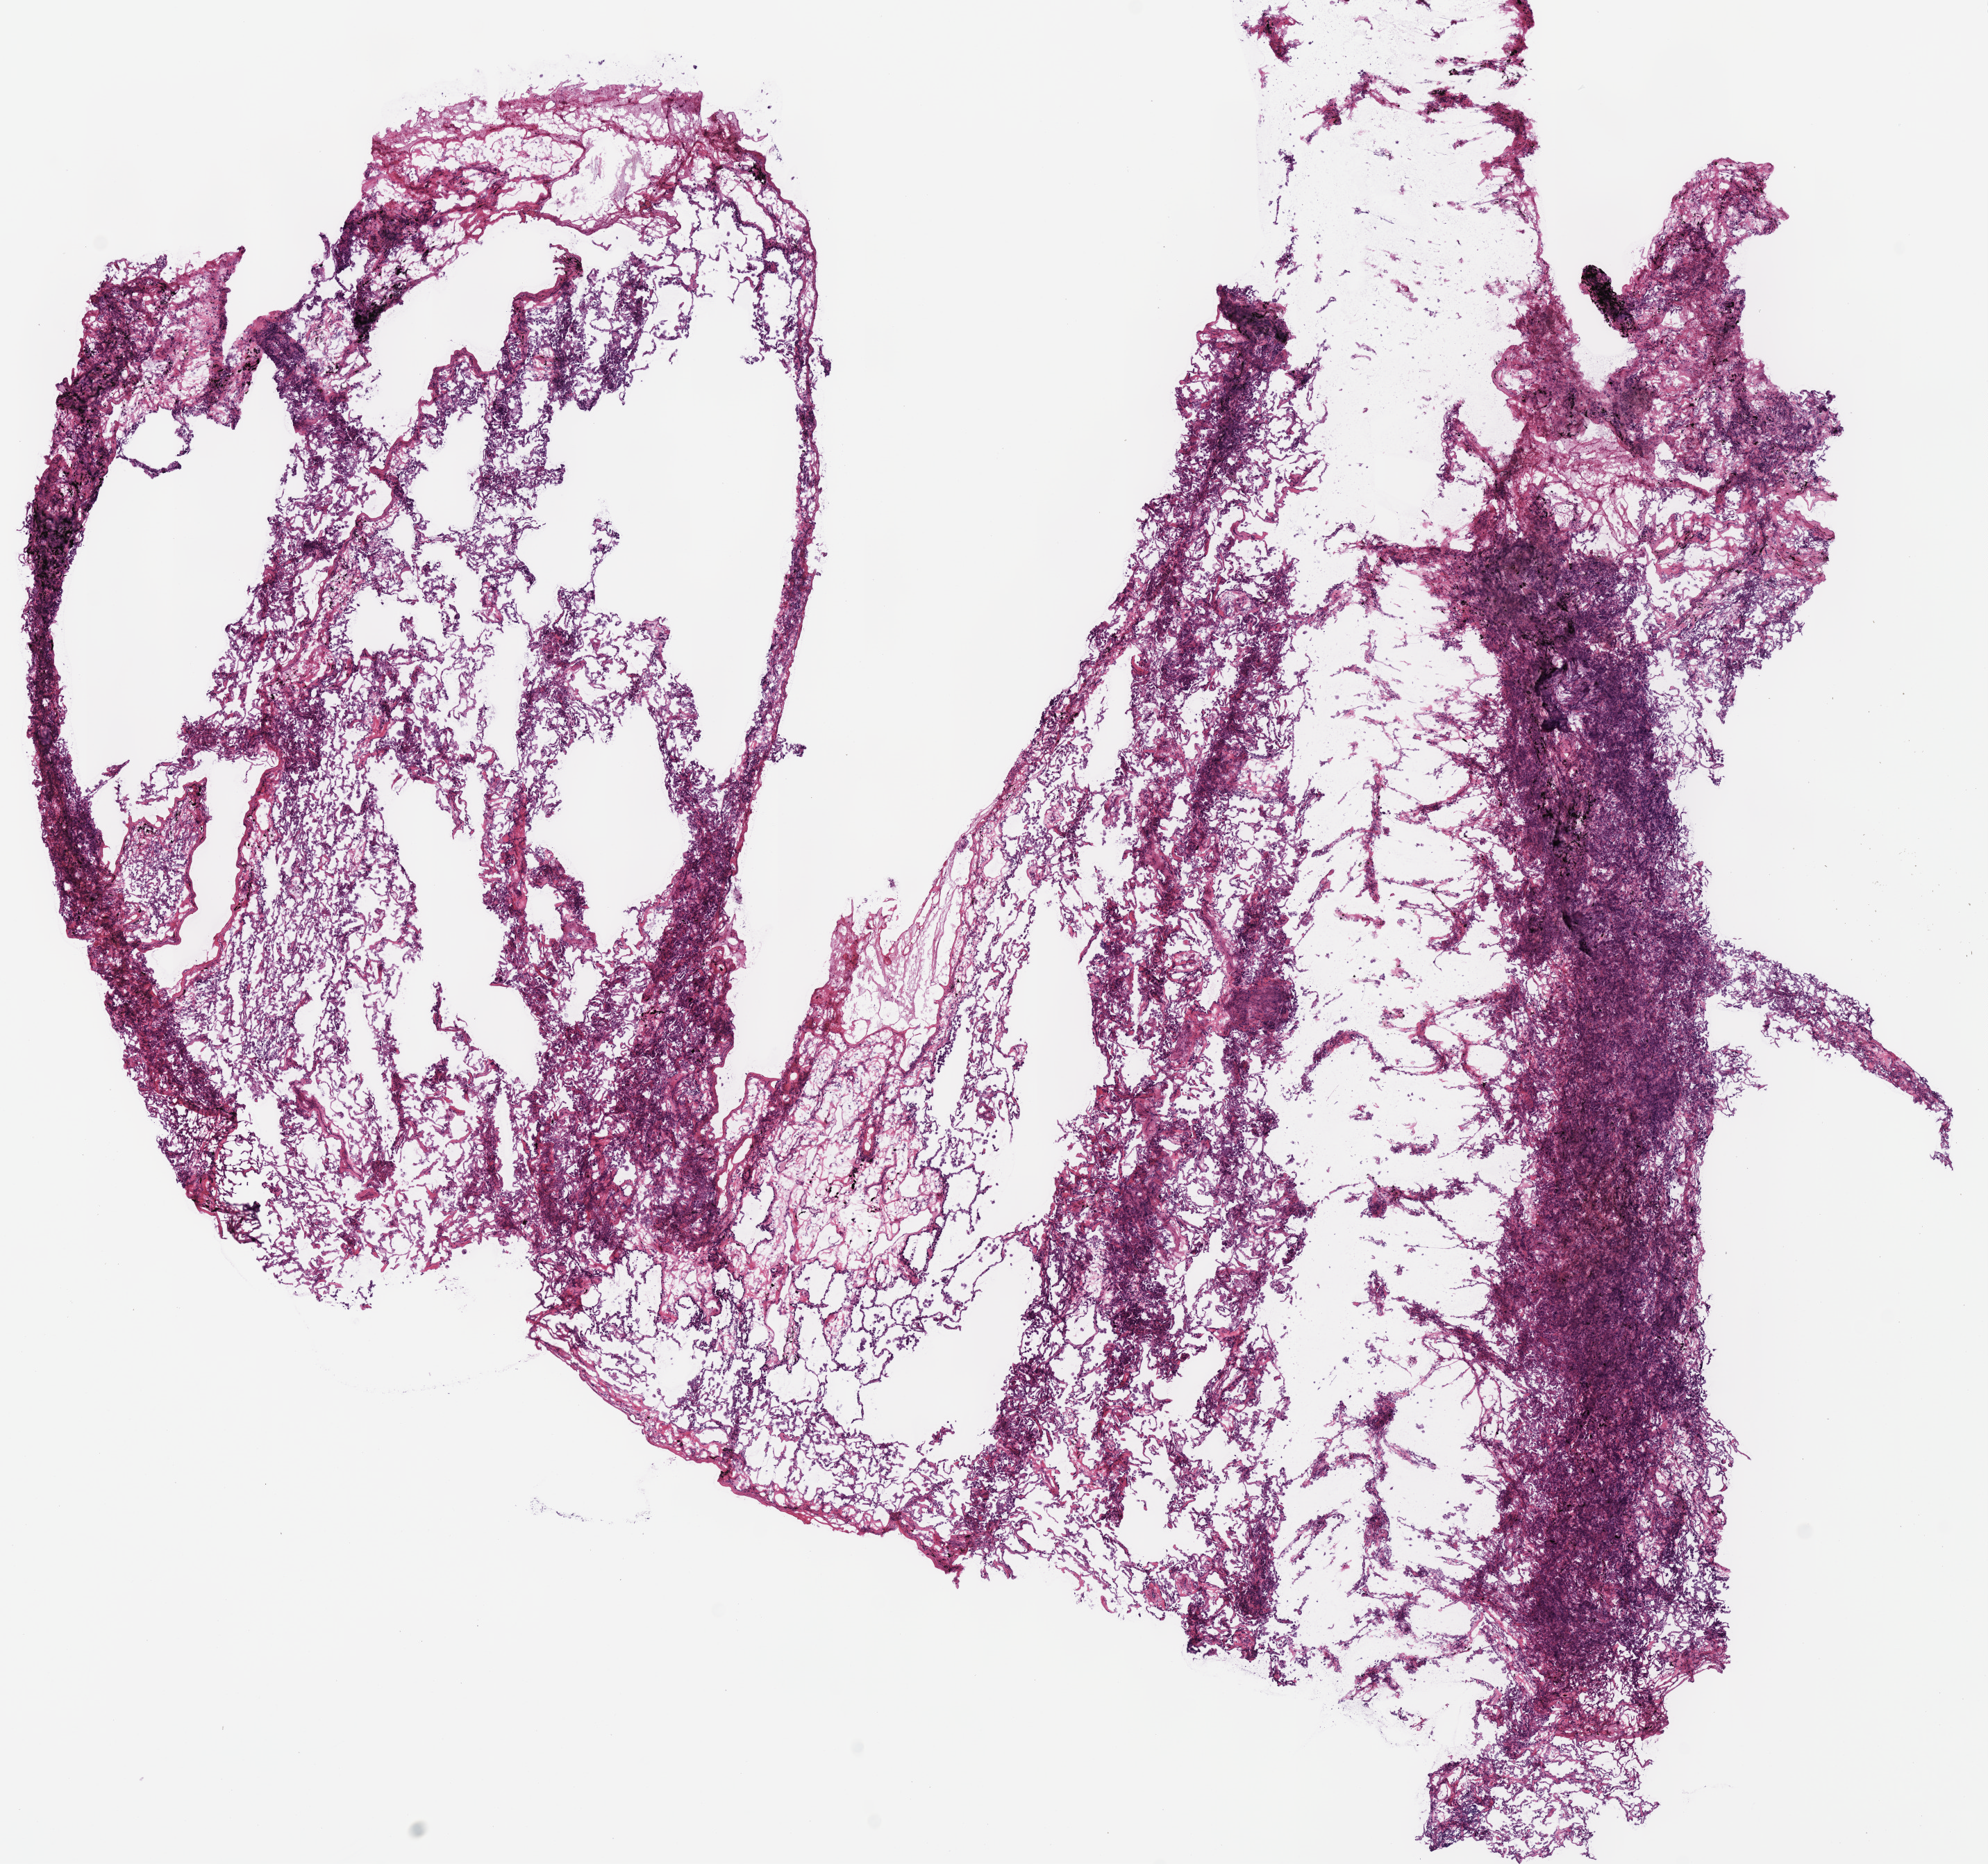
Whole-slide histology image, H&E-stained, whole scanned area (about 11.3 x 10.6 mm, slide scanned at 40x) shown as a low-resolution overview. Frozen section from the top of the tissue portion. Solid tissue normal (non-tumour tissue) sample from the lung. Male patient; age at initial diagnosis 70 years. Infiltration values recorded for this section: lymphocyte infiltration 1%, monocyte infiltration 15%, neutrophil infiltration 0%.
- this section: solid tissue normal (non-tumour) sample from the same patient
- patient diagnosis: Adenocarcinoma, NOS (lower lobe, lung)